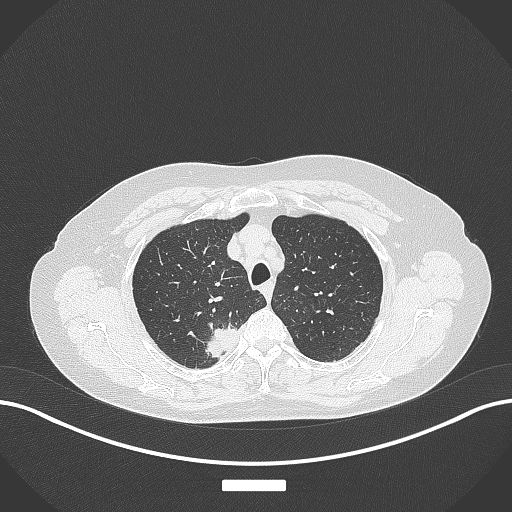
Chest CT, one axial slice. Lung window (W 1500 / L -600 HU). 1 mm slice thickness. 512 × 512 image matrix, field of view 400 × 400 mm. Female patient, age 62 years. Case-level facts recorded for this patient, not image findings: clinical TNM (as recorded): T1c N1 M0.
Outlined on this slice (bounding box drawn by a radiologist):
- lung tumour (recorded histology: squamous cell carcinoma): bounding box (x1, y1, x2, y2) in pixels: (202, 319, 241, 360)